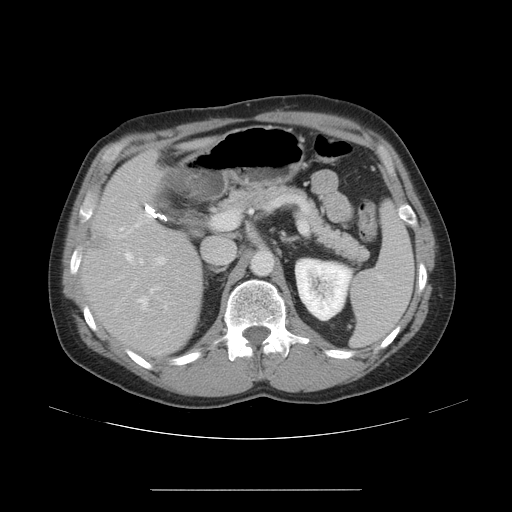
Contrast-enhanced abdominal CT, one axial slice. Position 27 of 48 along the scan axis. Reconstruction kernel STANDARD. 120 kVp. Intravenous contrast given. Soft-tissue window (W 400 / L 40 HU). 5 mm slice thickness. 512 × 512 image matrix, field of view 409 × 409 mm. Male patient, age 56 years. Case-level facts recorded for this patient, not image findings: diagnosis: colorectal cancer liver metastases, imaged before liver resection; multiple liver metastases: yes; largest metastasis: 1.8 cm.
Outlined on this slice (manually delineated by an expert):
- hepatic veins: bounding box (x1, y1, x2, y2) in pixels: (124, 178, 161, 311)
- liver: (84, 154, 202, 352)
- planned liver remnant (the part of the liver to remain after resection): (87, 154, 202, 352)
- portal vein (with intrahepatic branches): (118, 213, 221, 309)
- liver metastasis: (93, 237, 105, 250)